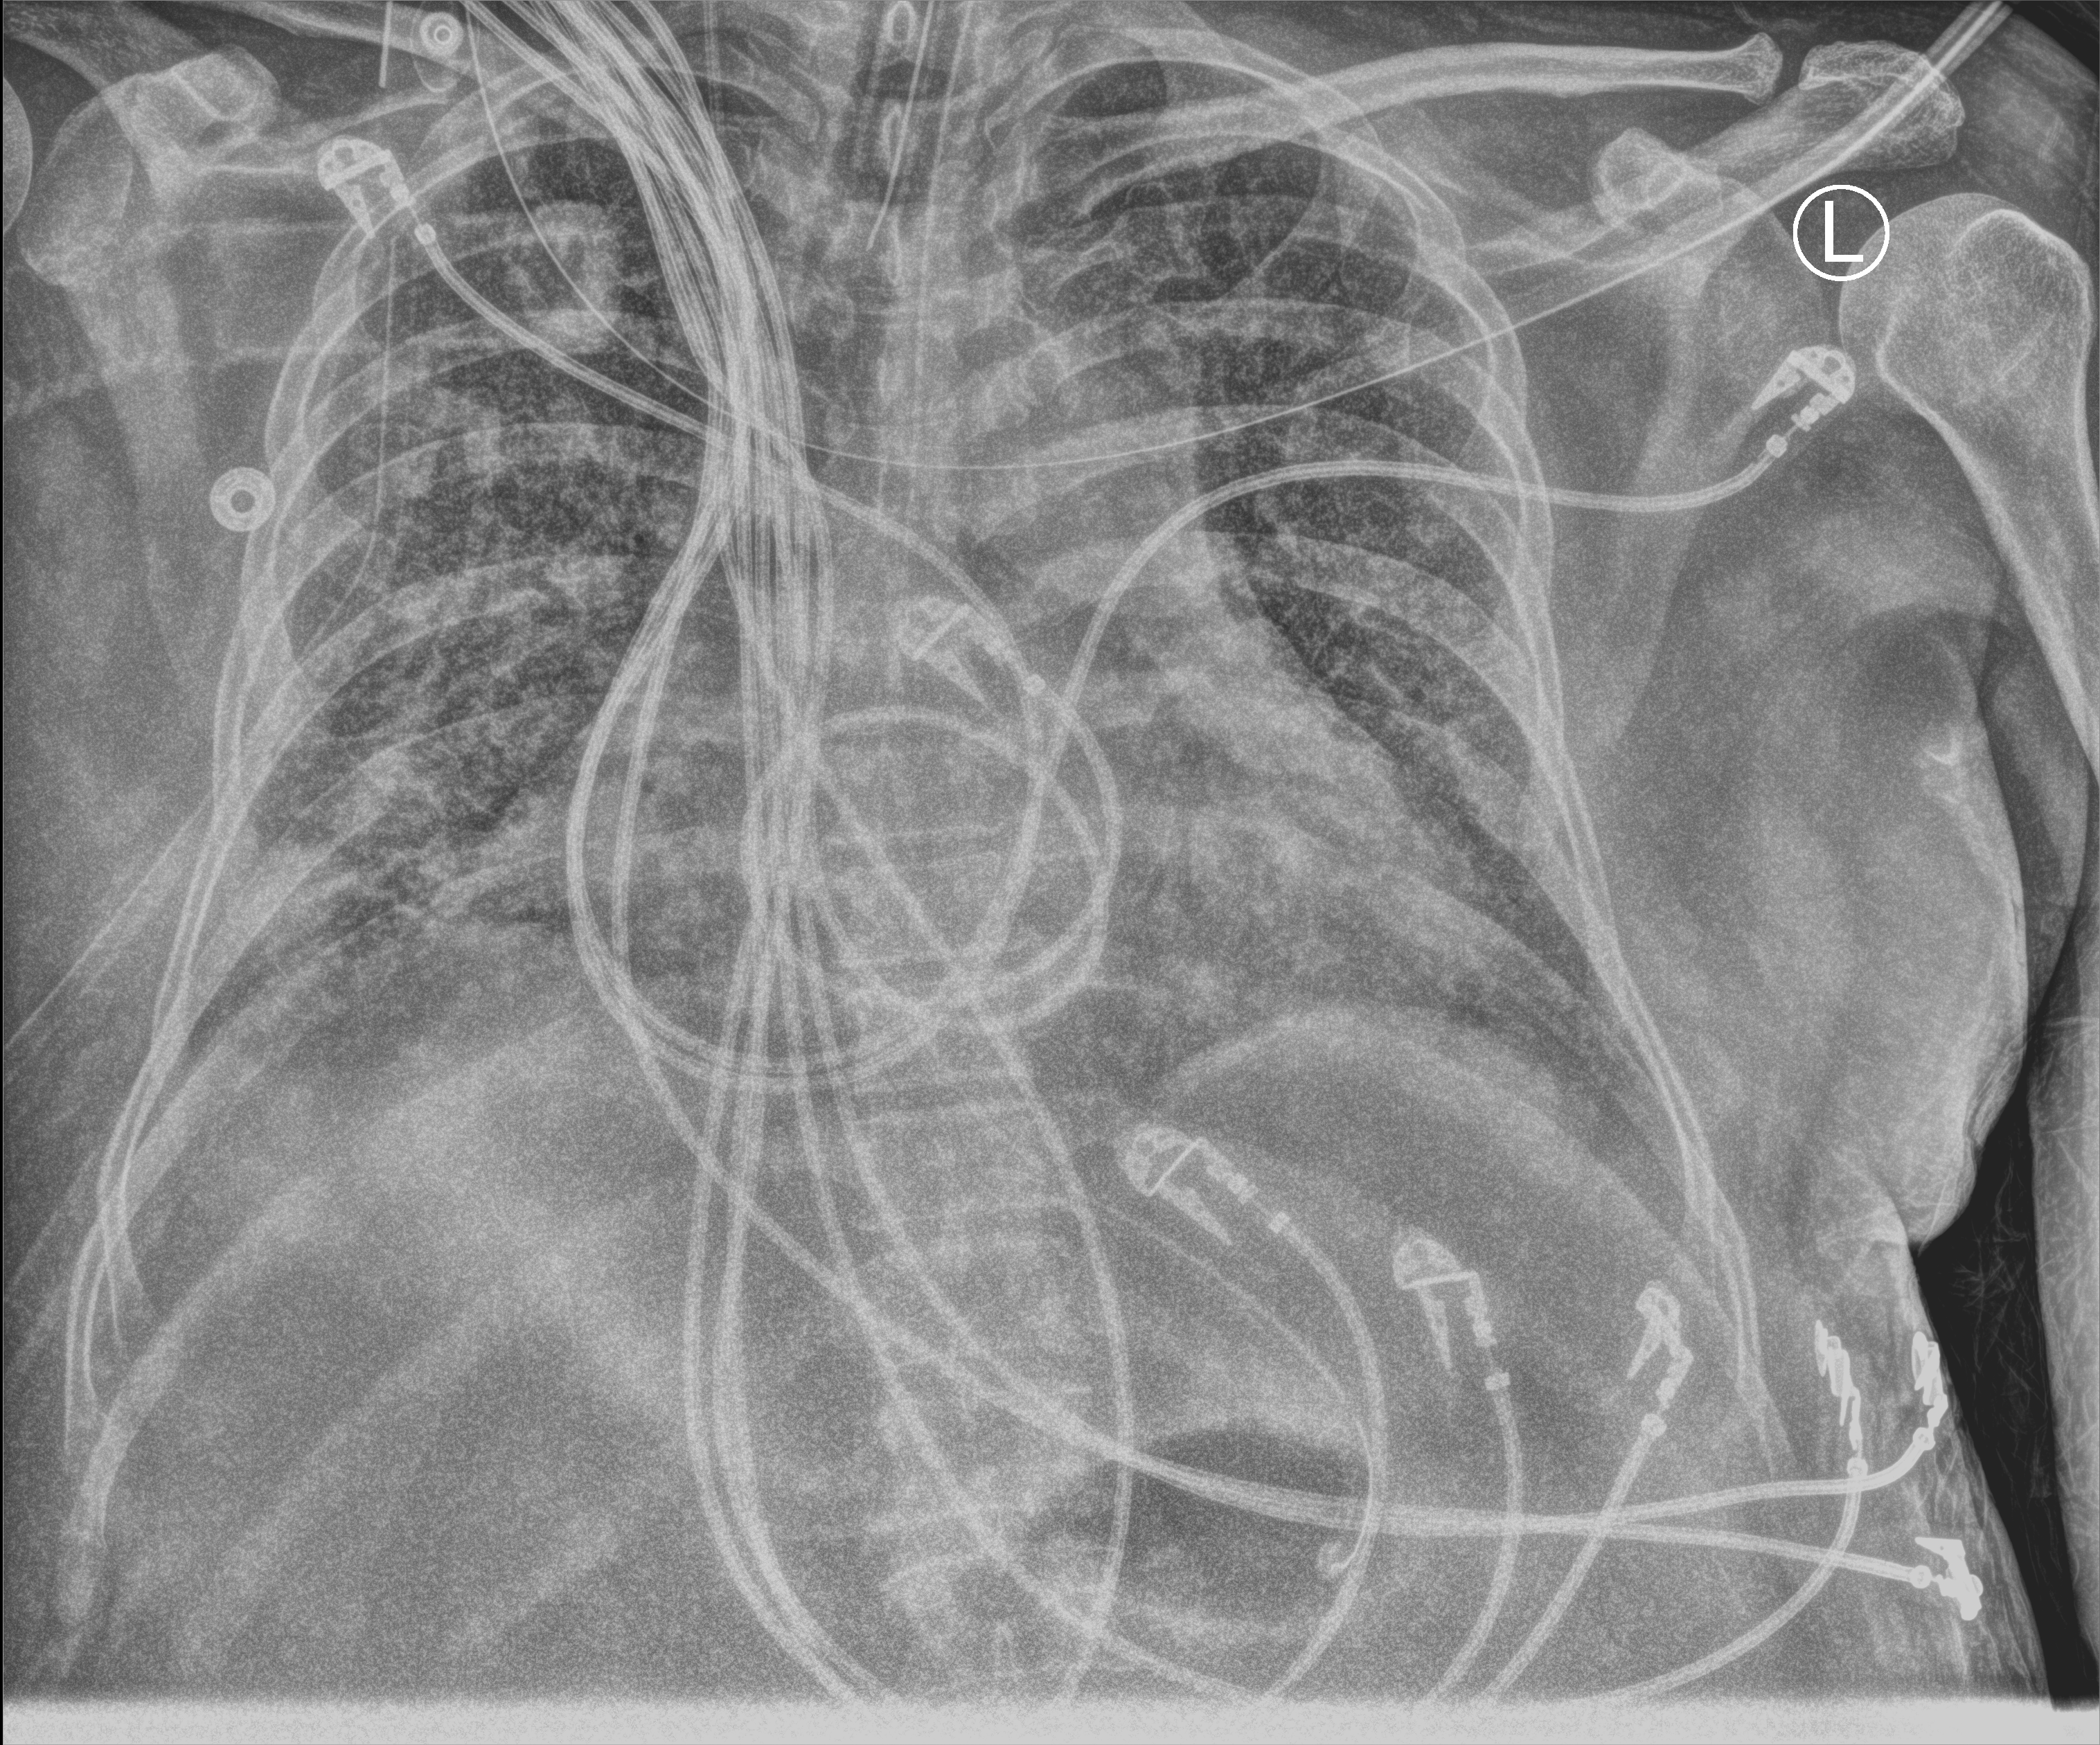
Portable chest radiograph, anteroposterior (AP) projection. Adult patient hospitalised with COVID-19, age 18–59 years.
From the hospital-stay record, not from the radiograph (when in the stay this image was taken is not recorded): mechanically ventilated during this hospital stay: yes; chronic kidney disease (admission record): no.